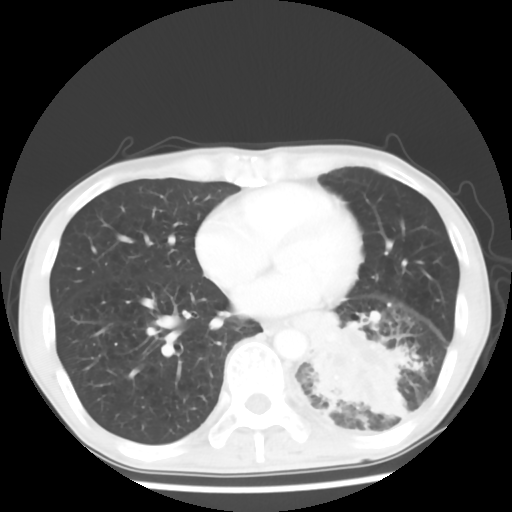
Chest CT, one axial slice; slice 24 of 64 in the series (ordered by position); reconstruction kernel STANDARD; 120 kVp; lung window (W 1500 / L -600 HU); 512 × 512 image matrix, field of view 313 × 313 mm. Patient: male, 68 years. Case-level facts recorded for this patient, not image findings: clinical TNM (as recorded): T4 N0 M0.
Annotated regions visible in this slice (rectangle marked by the reading radiologist):
- lung tumour (recorded histology: squamous cell carcinoma): box from (x=304, y=305) to (x=418, y=424) px